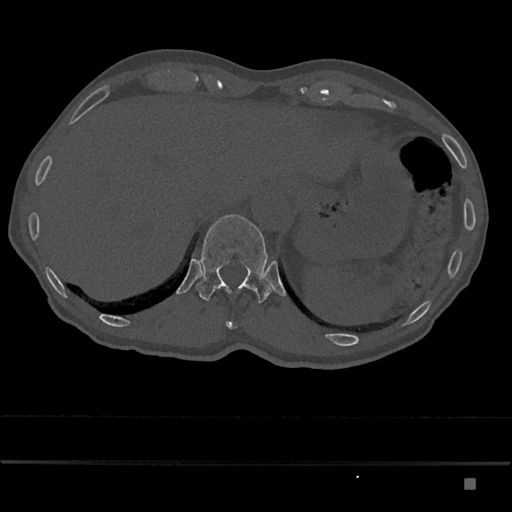
CT including the spine, one axial slice. Position 626 of 797 along the scan axis. Bone window (W 1800 / L 400 HU). 512 × 512 image matrix, field of view 390 × 390 mm. Male patient, age 72 years. From the clinical record (not read from this slice): primary cancer: prostate.
Structures marked on this image (semi-automatically segmented with operator editing):
- T11 vertebra: bounding box [x1, y1, x2, y2] px = [226, 321, 233, 328]
- T12 vertebra: [196, 214, 272, 303]